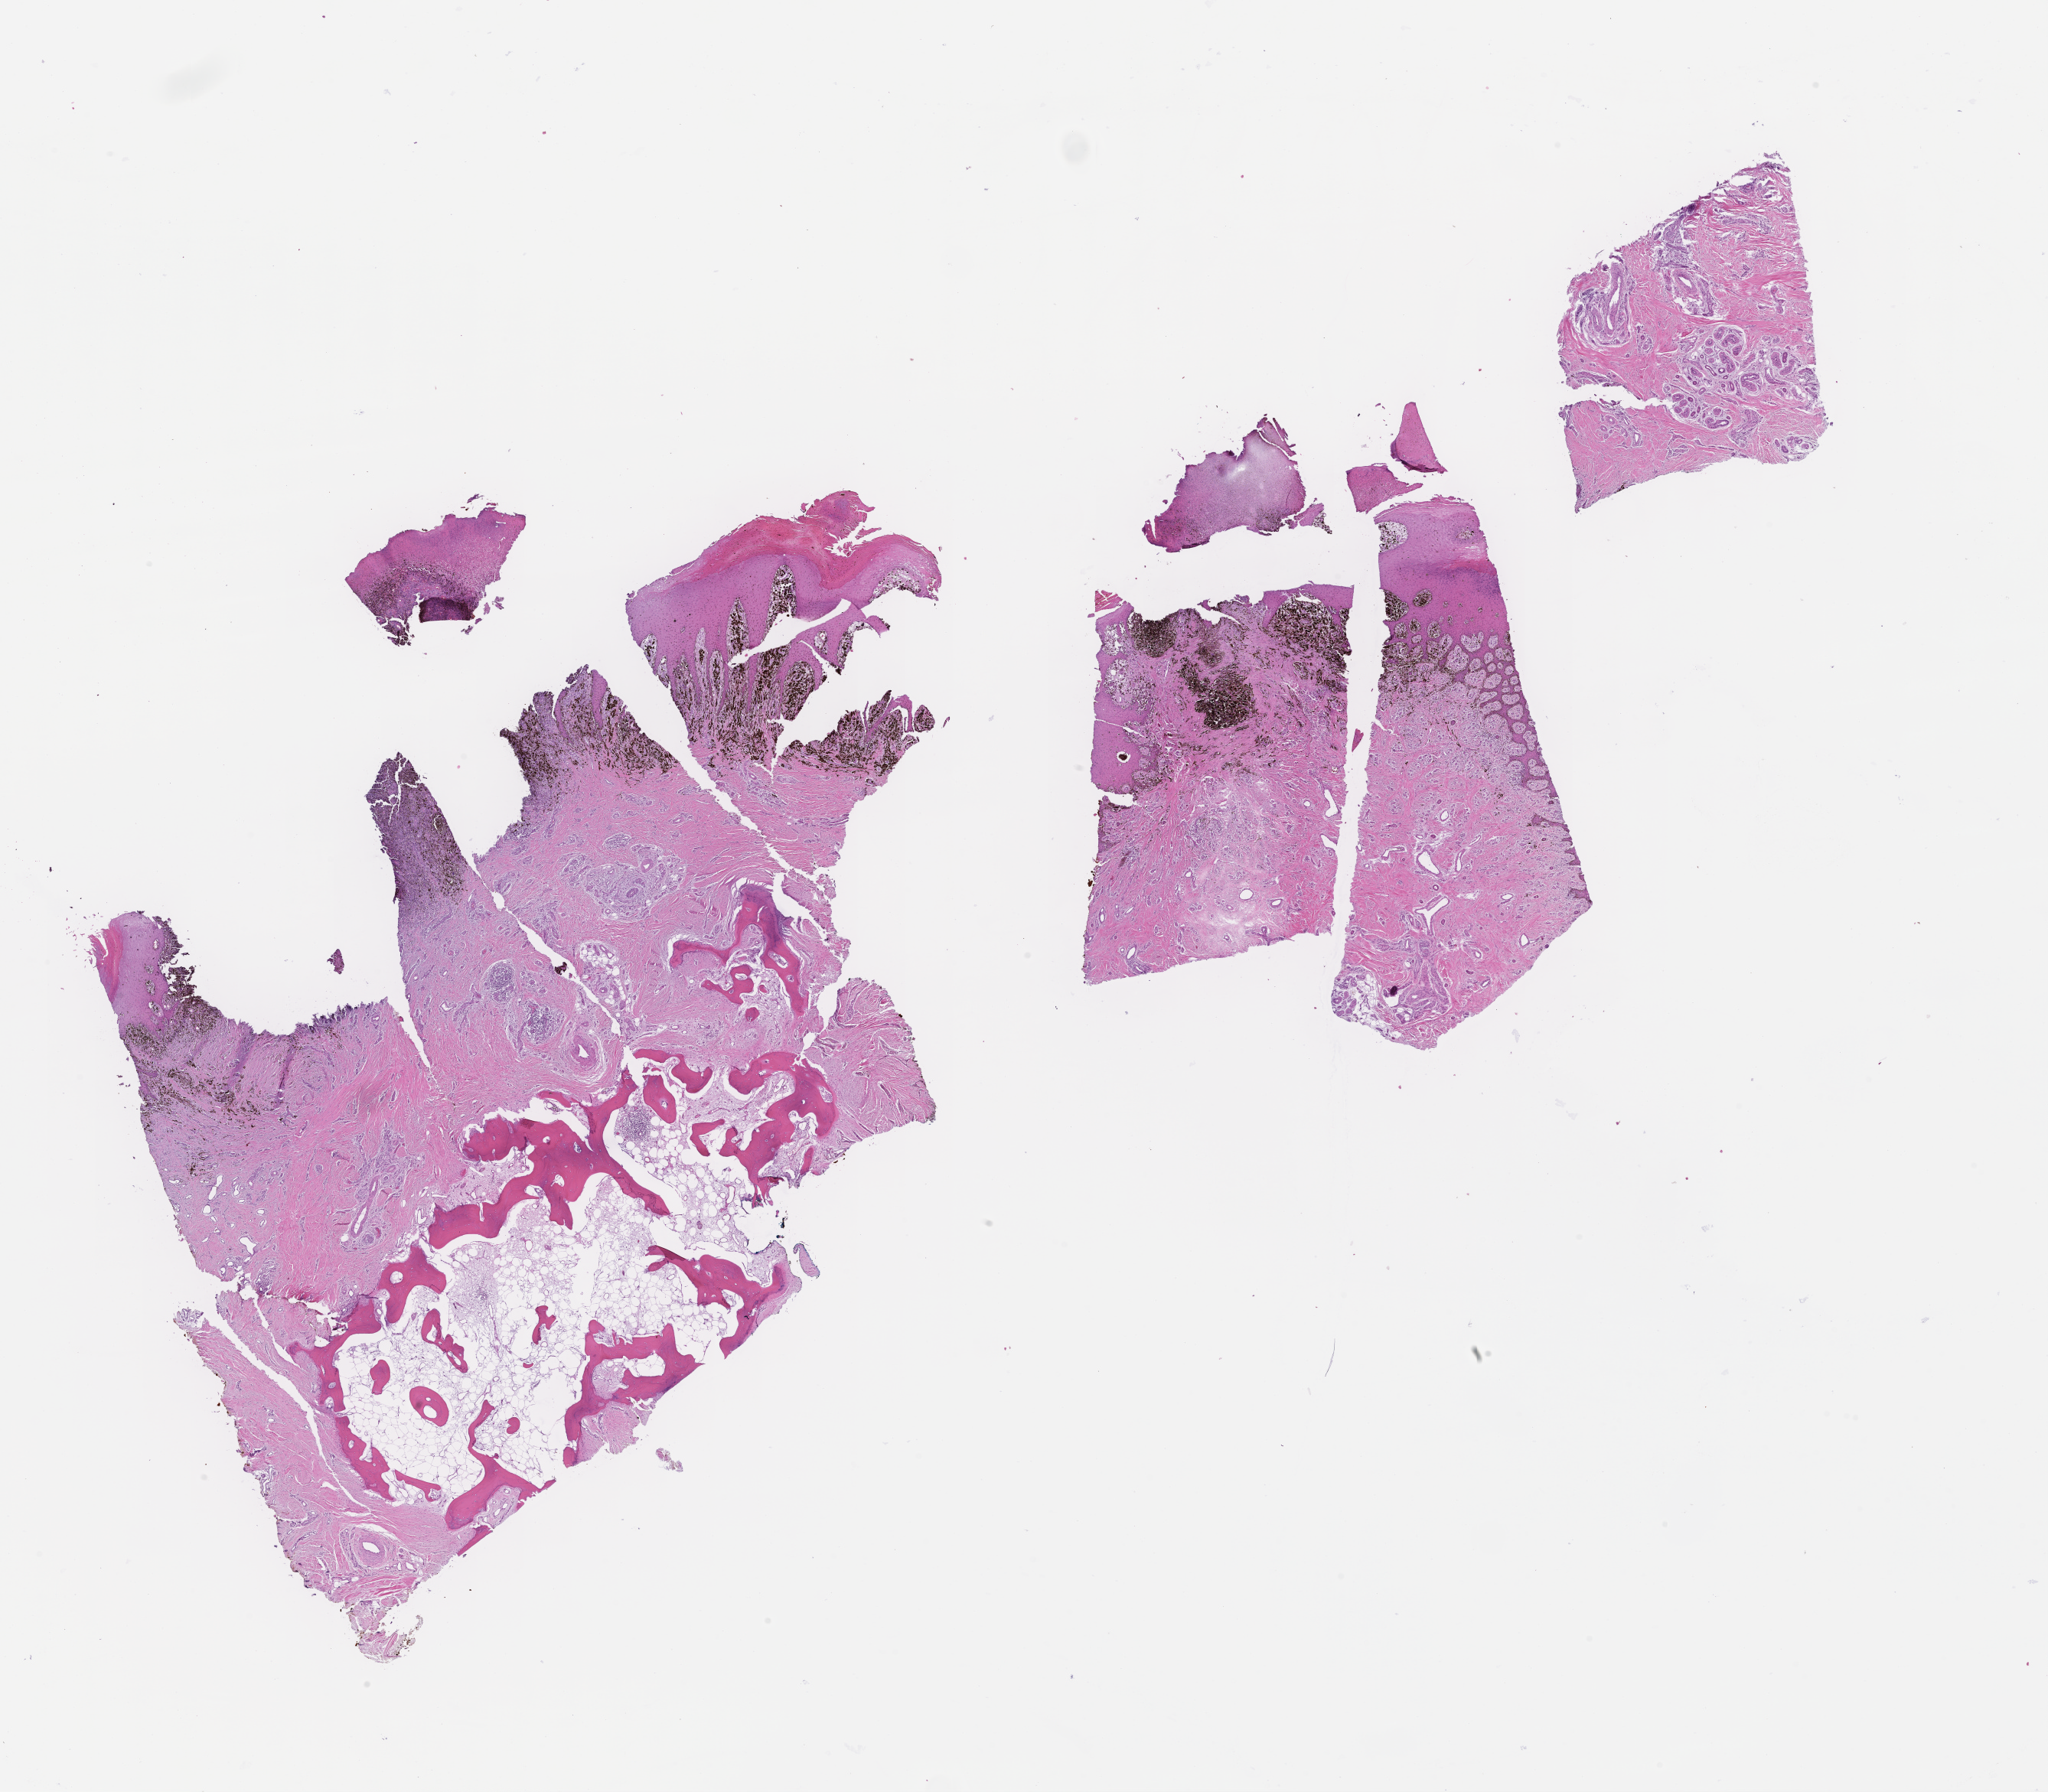
Whole-slide image, hematoxylin and eosin (H&E) stain, shown as a low-resolution overview of the whole scanned area (about 21.6 x 18.9 mm). FFPE section. Tissue site: skin. Specimen time point: archival tissue. Patient: male.
This section: primary tumour tissue. Diagnosis: Melanoma.